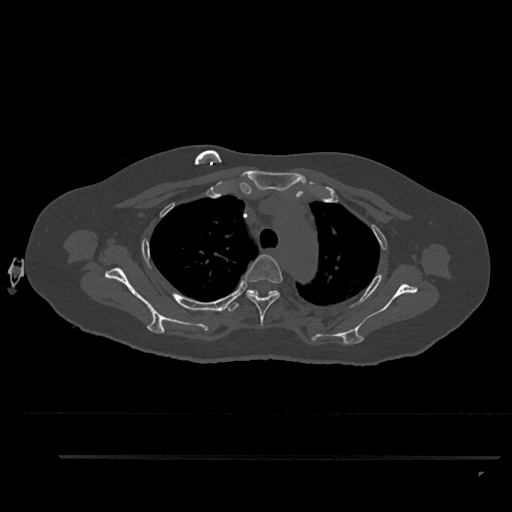
CT including the spine, one axial slice; slice 672 of 797 in the series (ordered by position); reconstruction kernel Br40s/3; bone window (W 1800 / L 400 HU); 0.5 mm slice thickness; 512 × 512 image matrix. Patient: female, 44 years. From the clinical record (not read from this slice): primary cancer: renal.
Structures marked on this image (semi-automatic segmentation, software-assisted and operator-edited):
- T3 vertebra: box from (x=244, y=254) to (x=283, y=326) px
- T4 vertebra: (x=227, y=289)–(x=279, y=312)